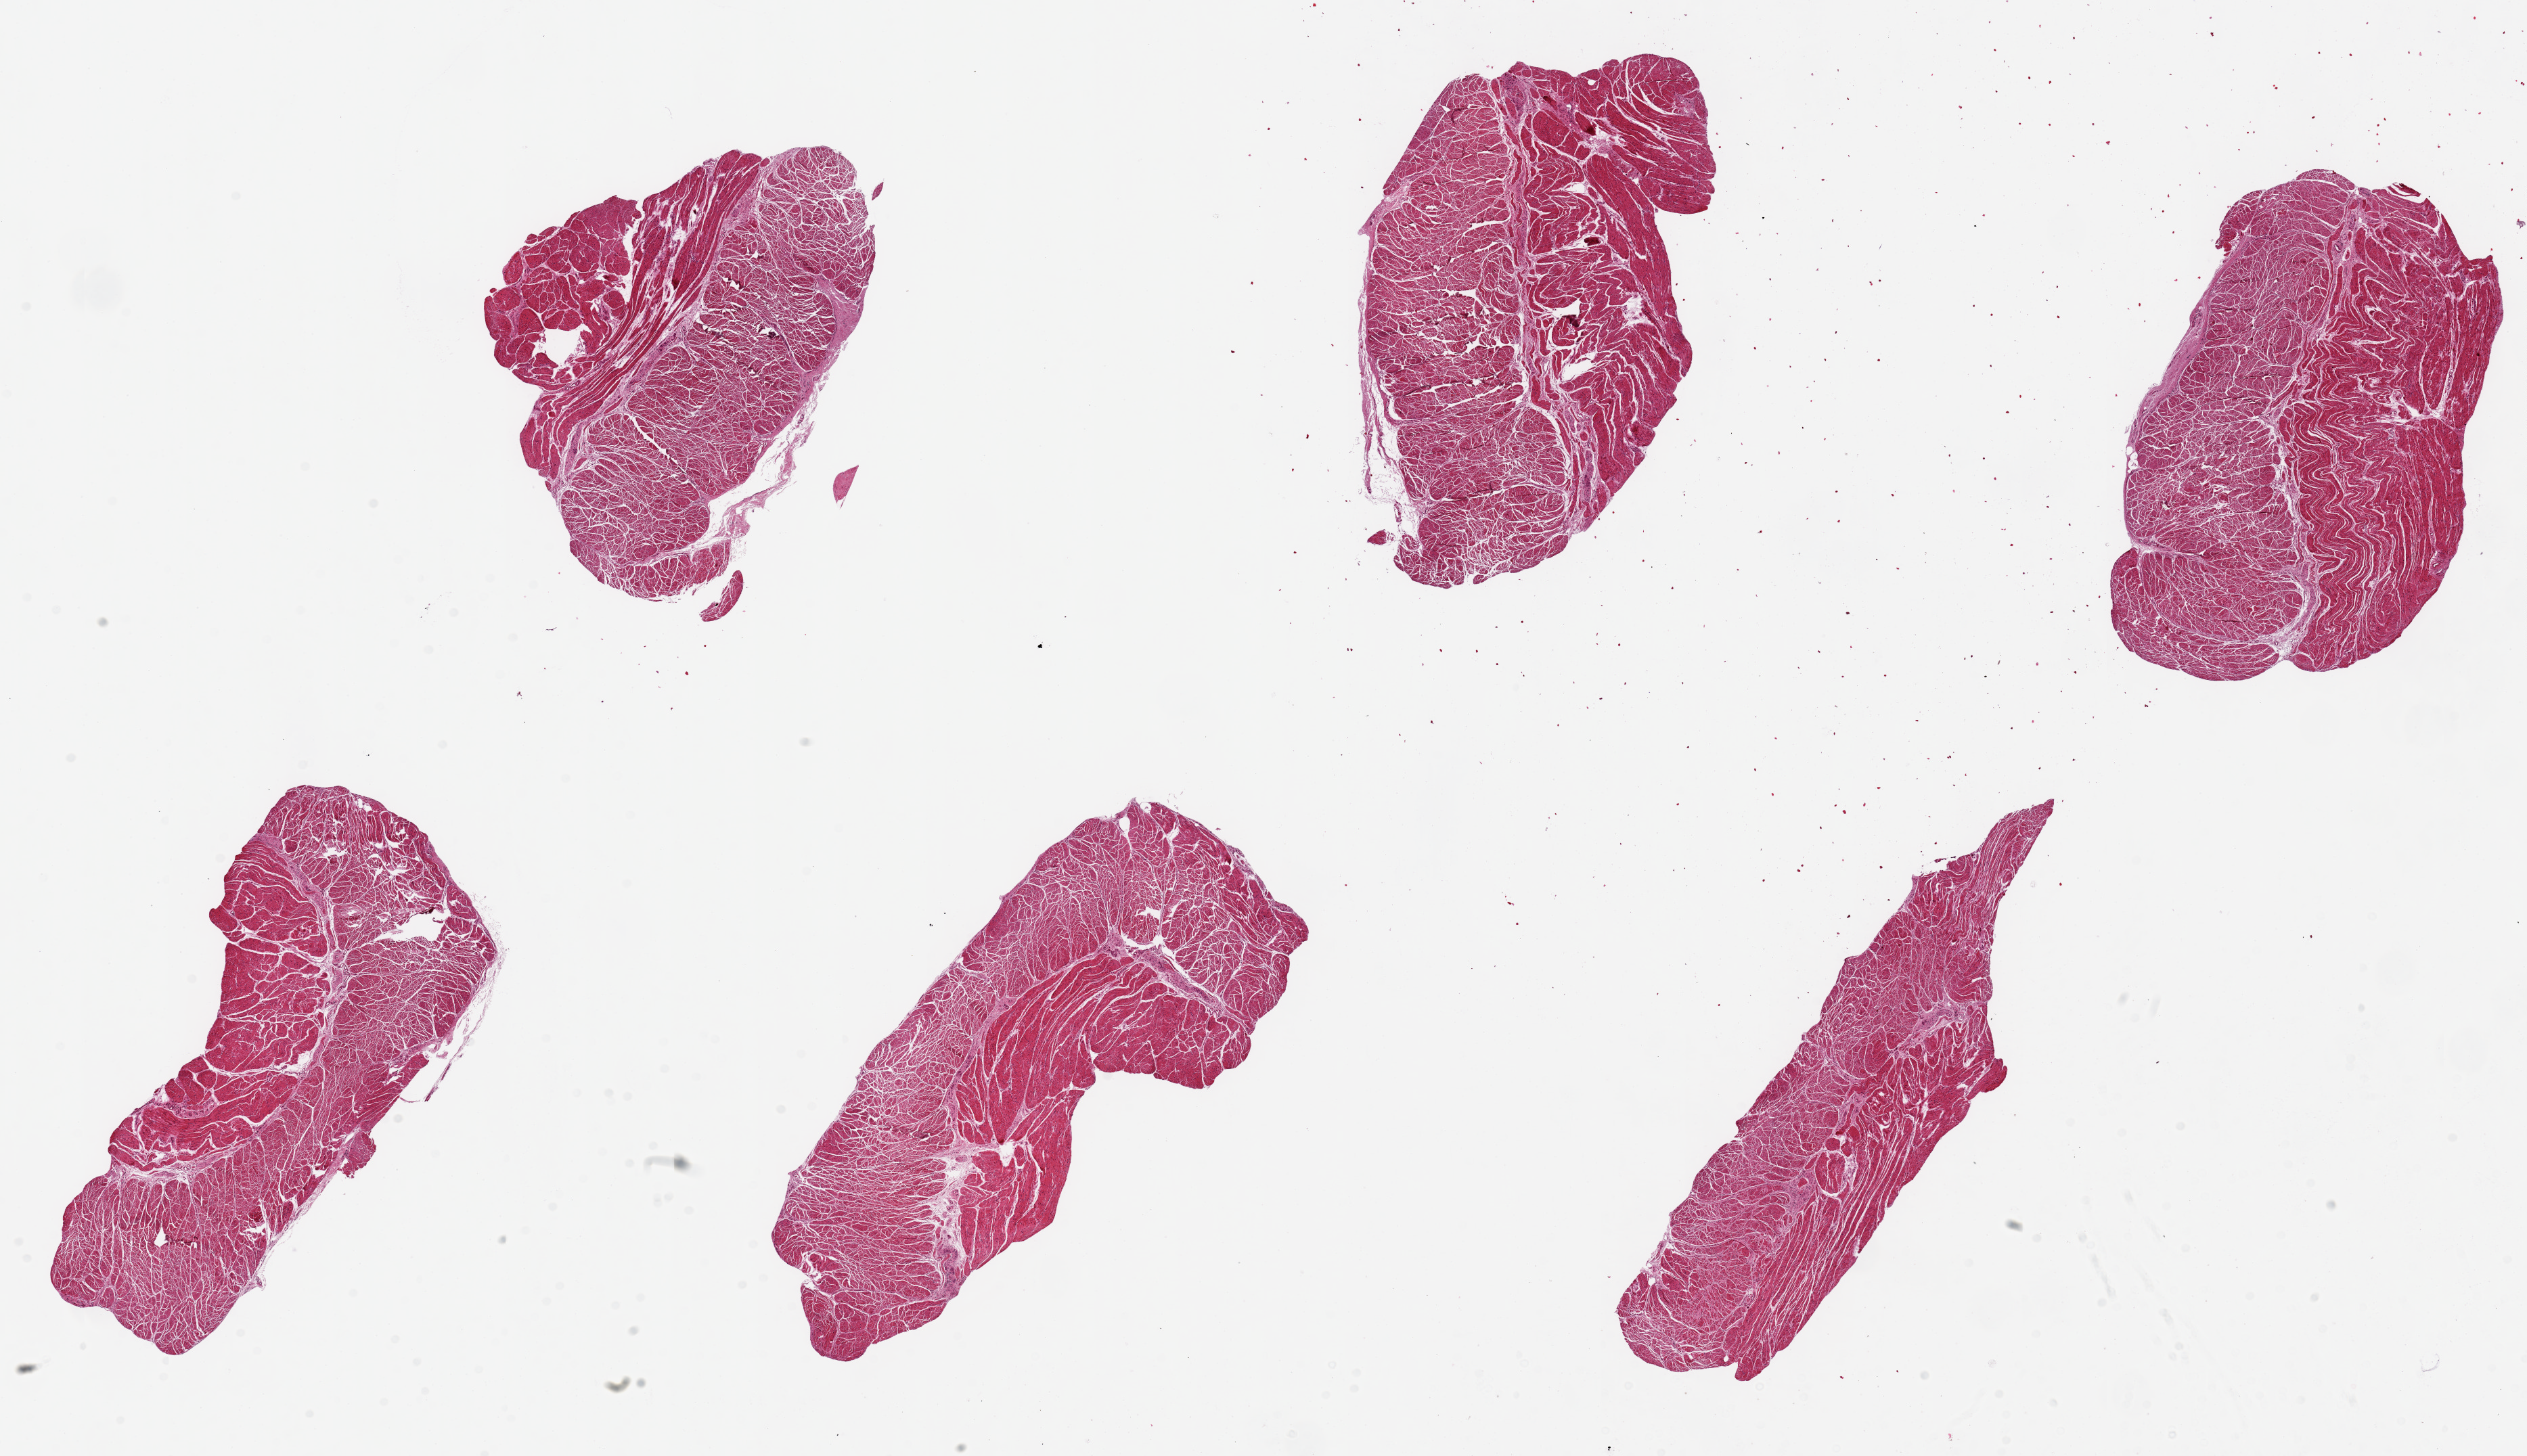
Whole-slide image, hematoxylin and eosin (H&E) stain, brightfield, whole scanned area (about 29.5 x 17.0 mm, acquisition: 20x scan) shown as a low-resolution overview. PAXgene-fixed paraffin-embedded (PFPE) section. Target tissue: gastroesophageal junction. Donor tissue sample. Donor: female.
- review note (as recorded): 6 pieces, up to 8x2mm; all muscularis; good specimens